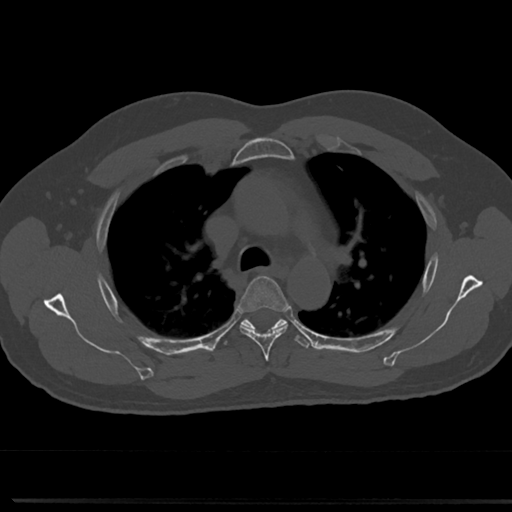
CT including the spine, one axial slice; reconstruction kernel Br40s/3; bone window (W 1800 / L 400 HU); 512 × 512 image matrix, field of view 355 × 355 mm. Male patient, age 61 years. Case-level facts recorded for this patient, not image findings: primary cancer: prostate.
Structures marked on this image (semi-automatic segmentation, software-assisted and operator-edited):
- T4 vertebra: box from (x=239, y=276) to (x=289, y=357) px
- T5 vertebra: (x=243, y=320)–(x=285, y=328)